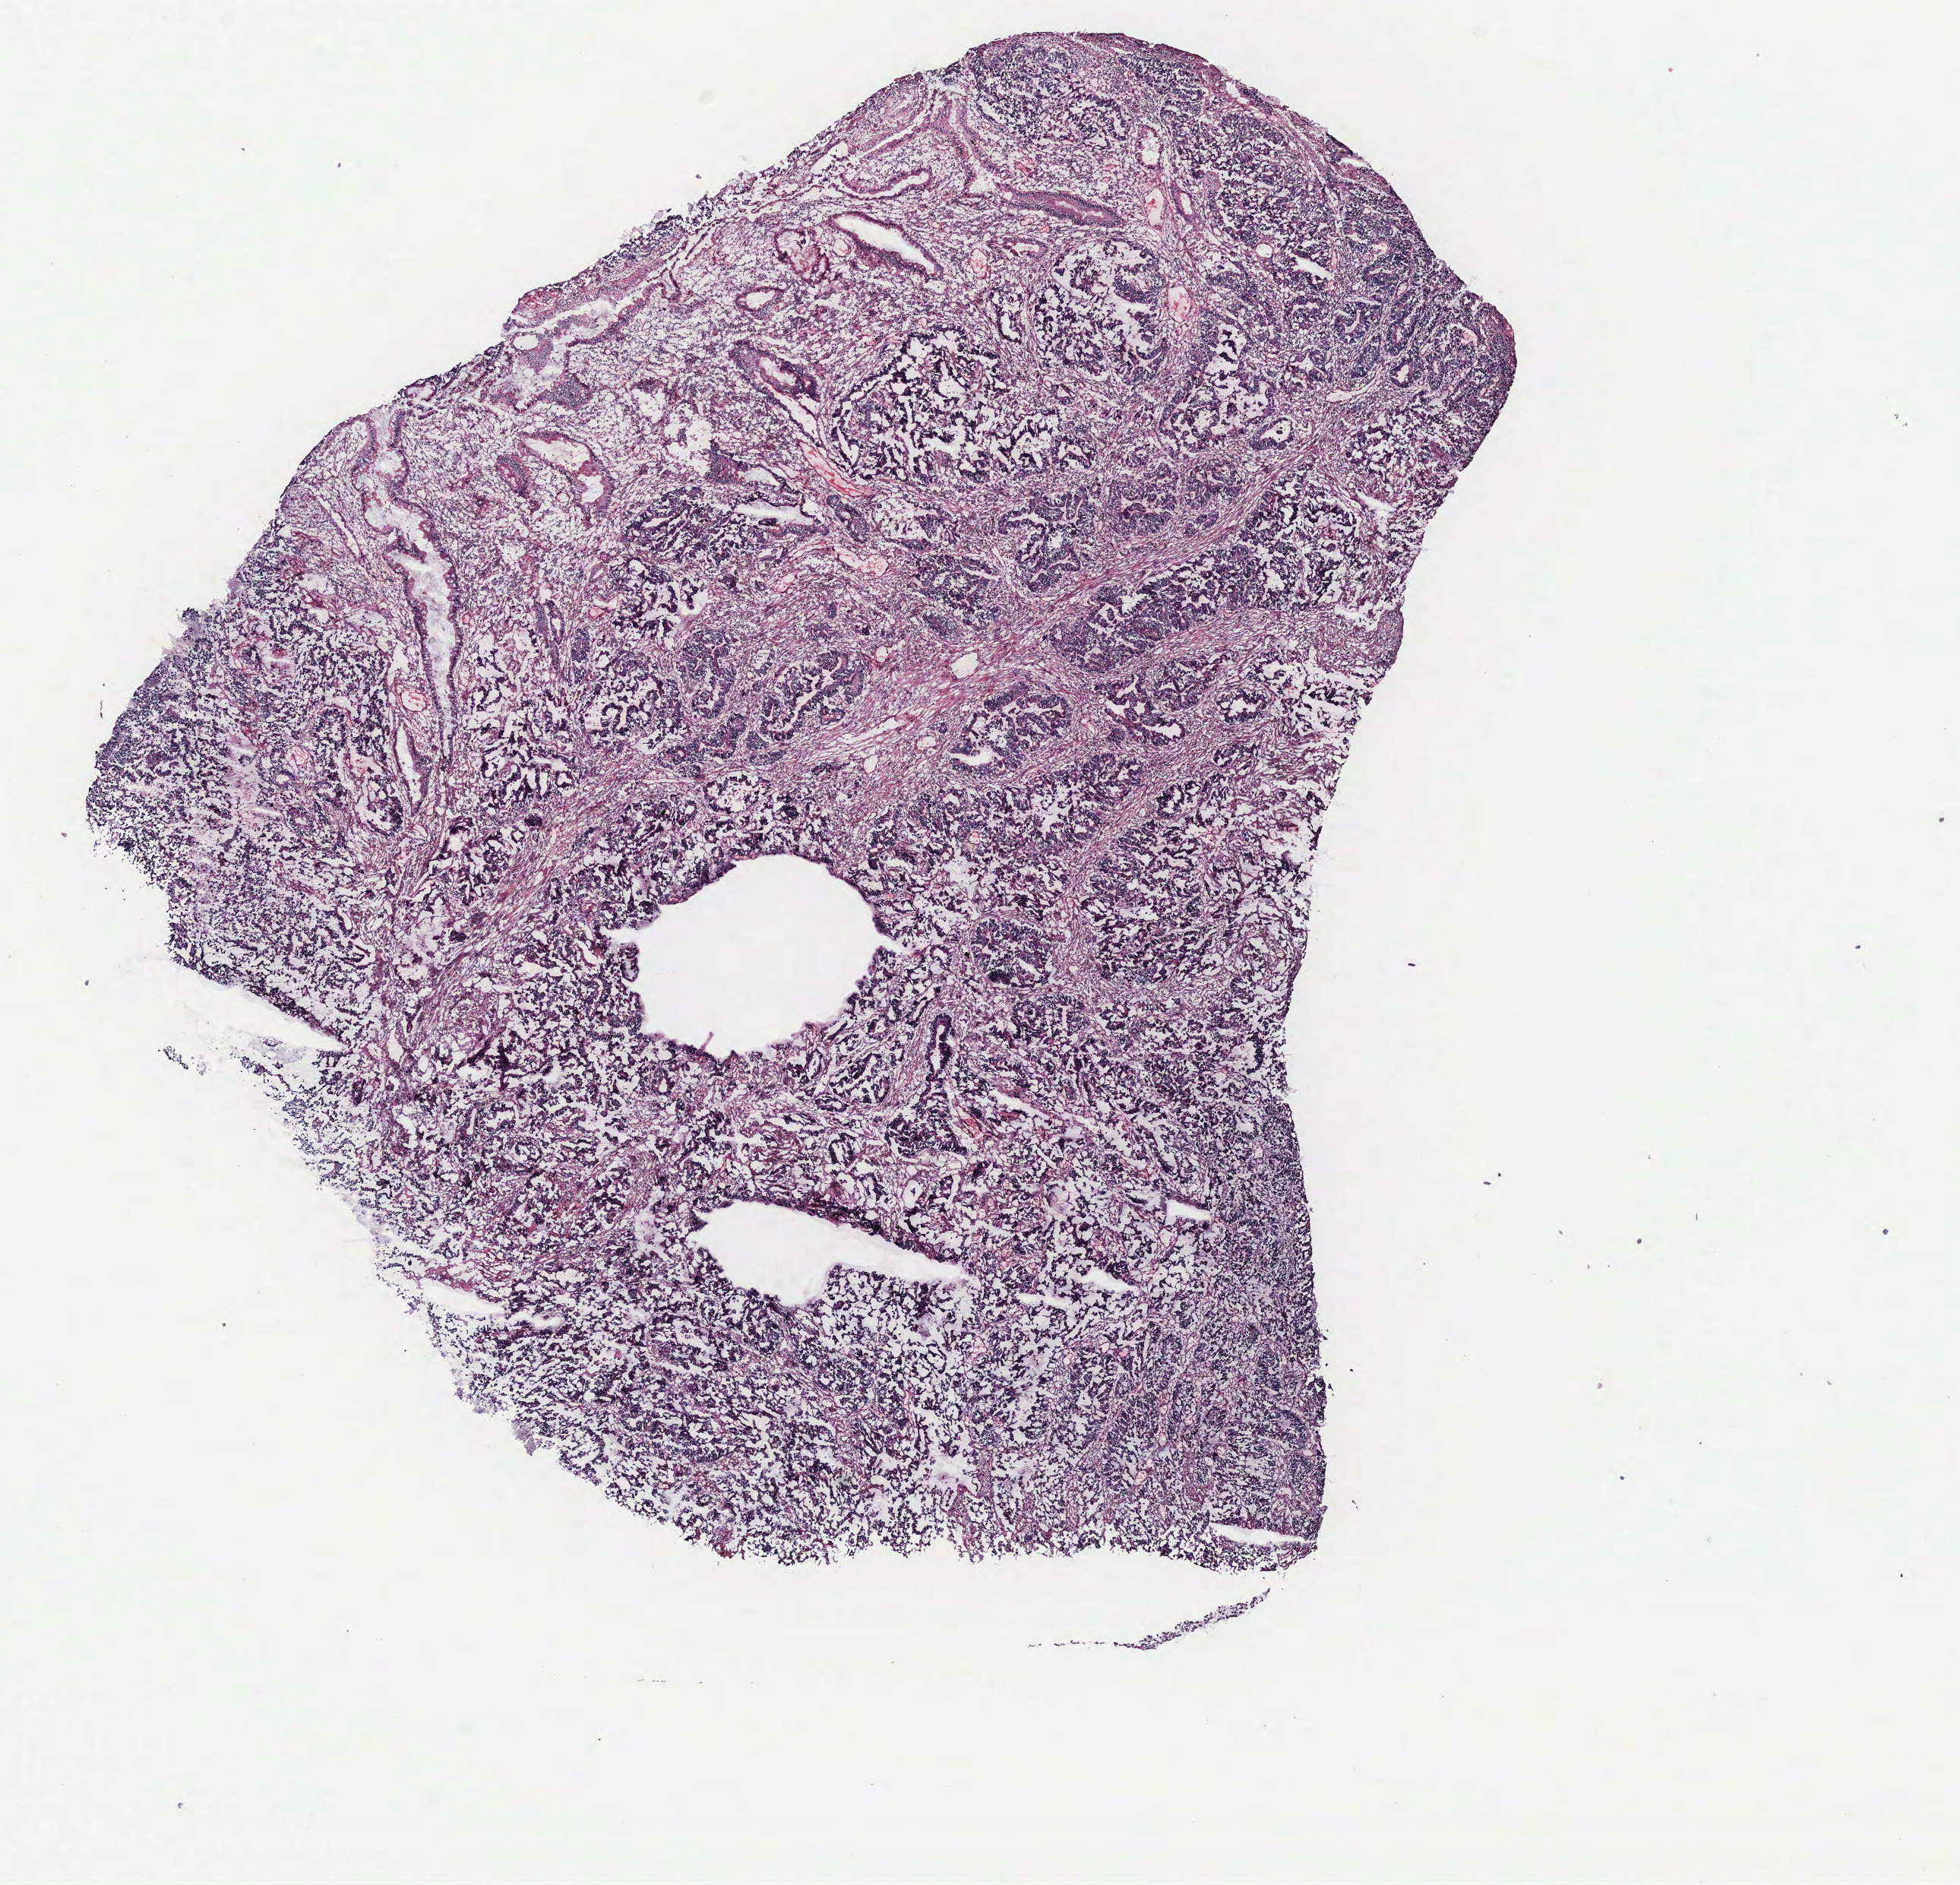
H&E-stained whole-slide image — shown as a low-resolution overview of the whole scanned area (about 10.3 x 9.9 mm, acquisition: 40x scan); colon, tissue type not recorded. Patient sex: female.
- patient diagnosis: Adenocarcinoma, NOS